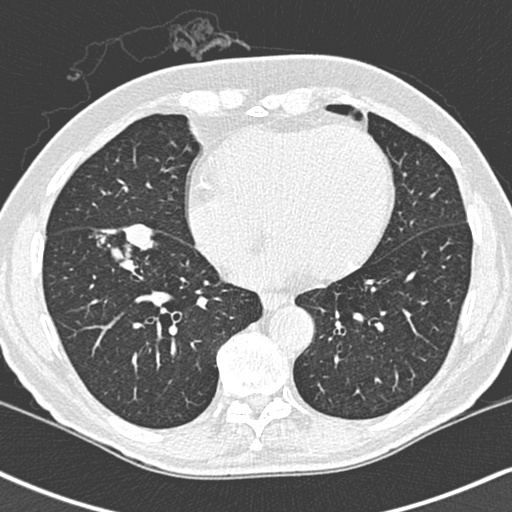
Low-dose screening chest CT, one axial slice; 120 kVp; lung window (W 1500 / L -600 HU); 1.3 mm slice thickness; 512 × 512 image matrix, field of view 323 × 323 mm.
Structures marked on this image (expert manual segmentation):
- lesion 1 (tumor, lower lobe of right lung): bounding box <90,186,156,234> (left, top, right, bottom; pixels)